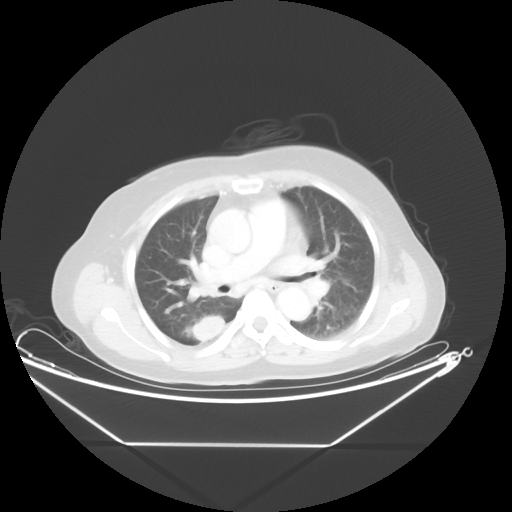
Chest CT, one axial slice. 100 kVp. Lung window (W 1500 / L -600 HU). 512 × 512 image matrix, field of view 462 × 462 mm. Female patient, age 62 years. From the clinical record (not read from this slice): clinical TNM (as recorded): T1c N0 M0; histopathological grade: G2-3.
Structures marked on this image (rectangle marked by the reading radiologist):
- lung tumour (recorded histology: adenocarcinoma): box from (x=184, y=309) to (x=233, y=356) px